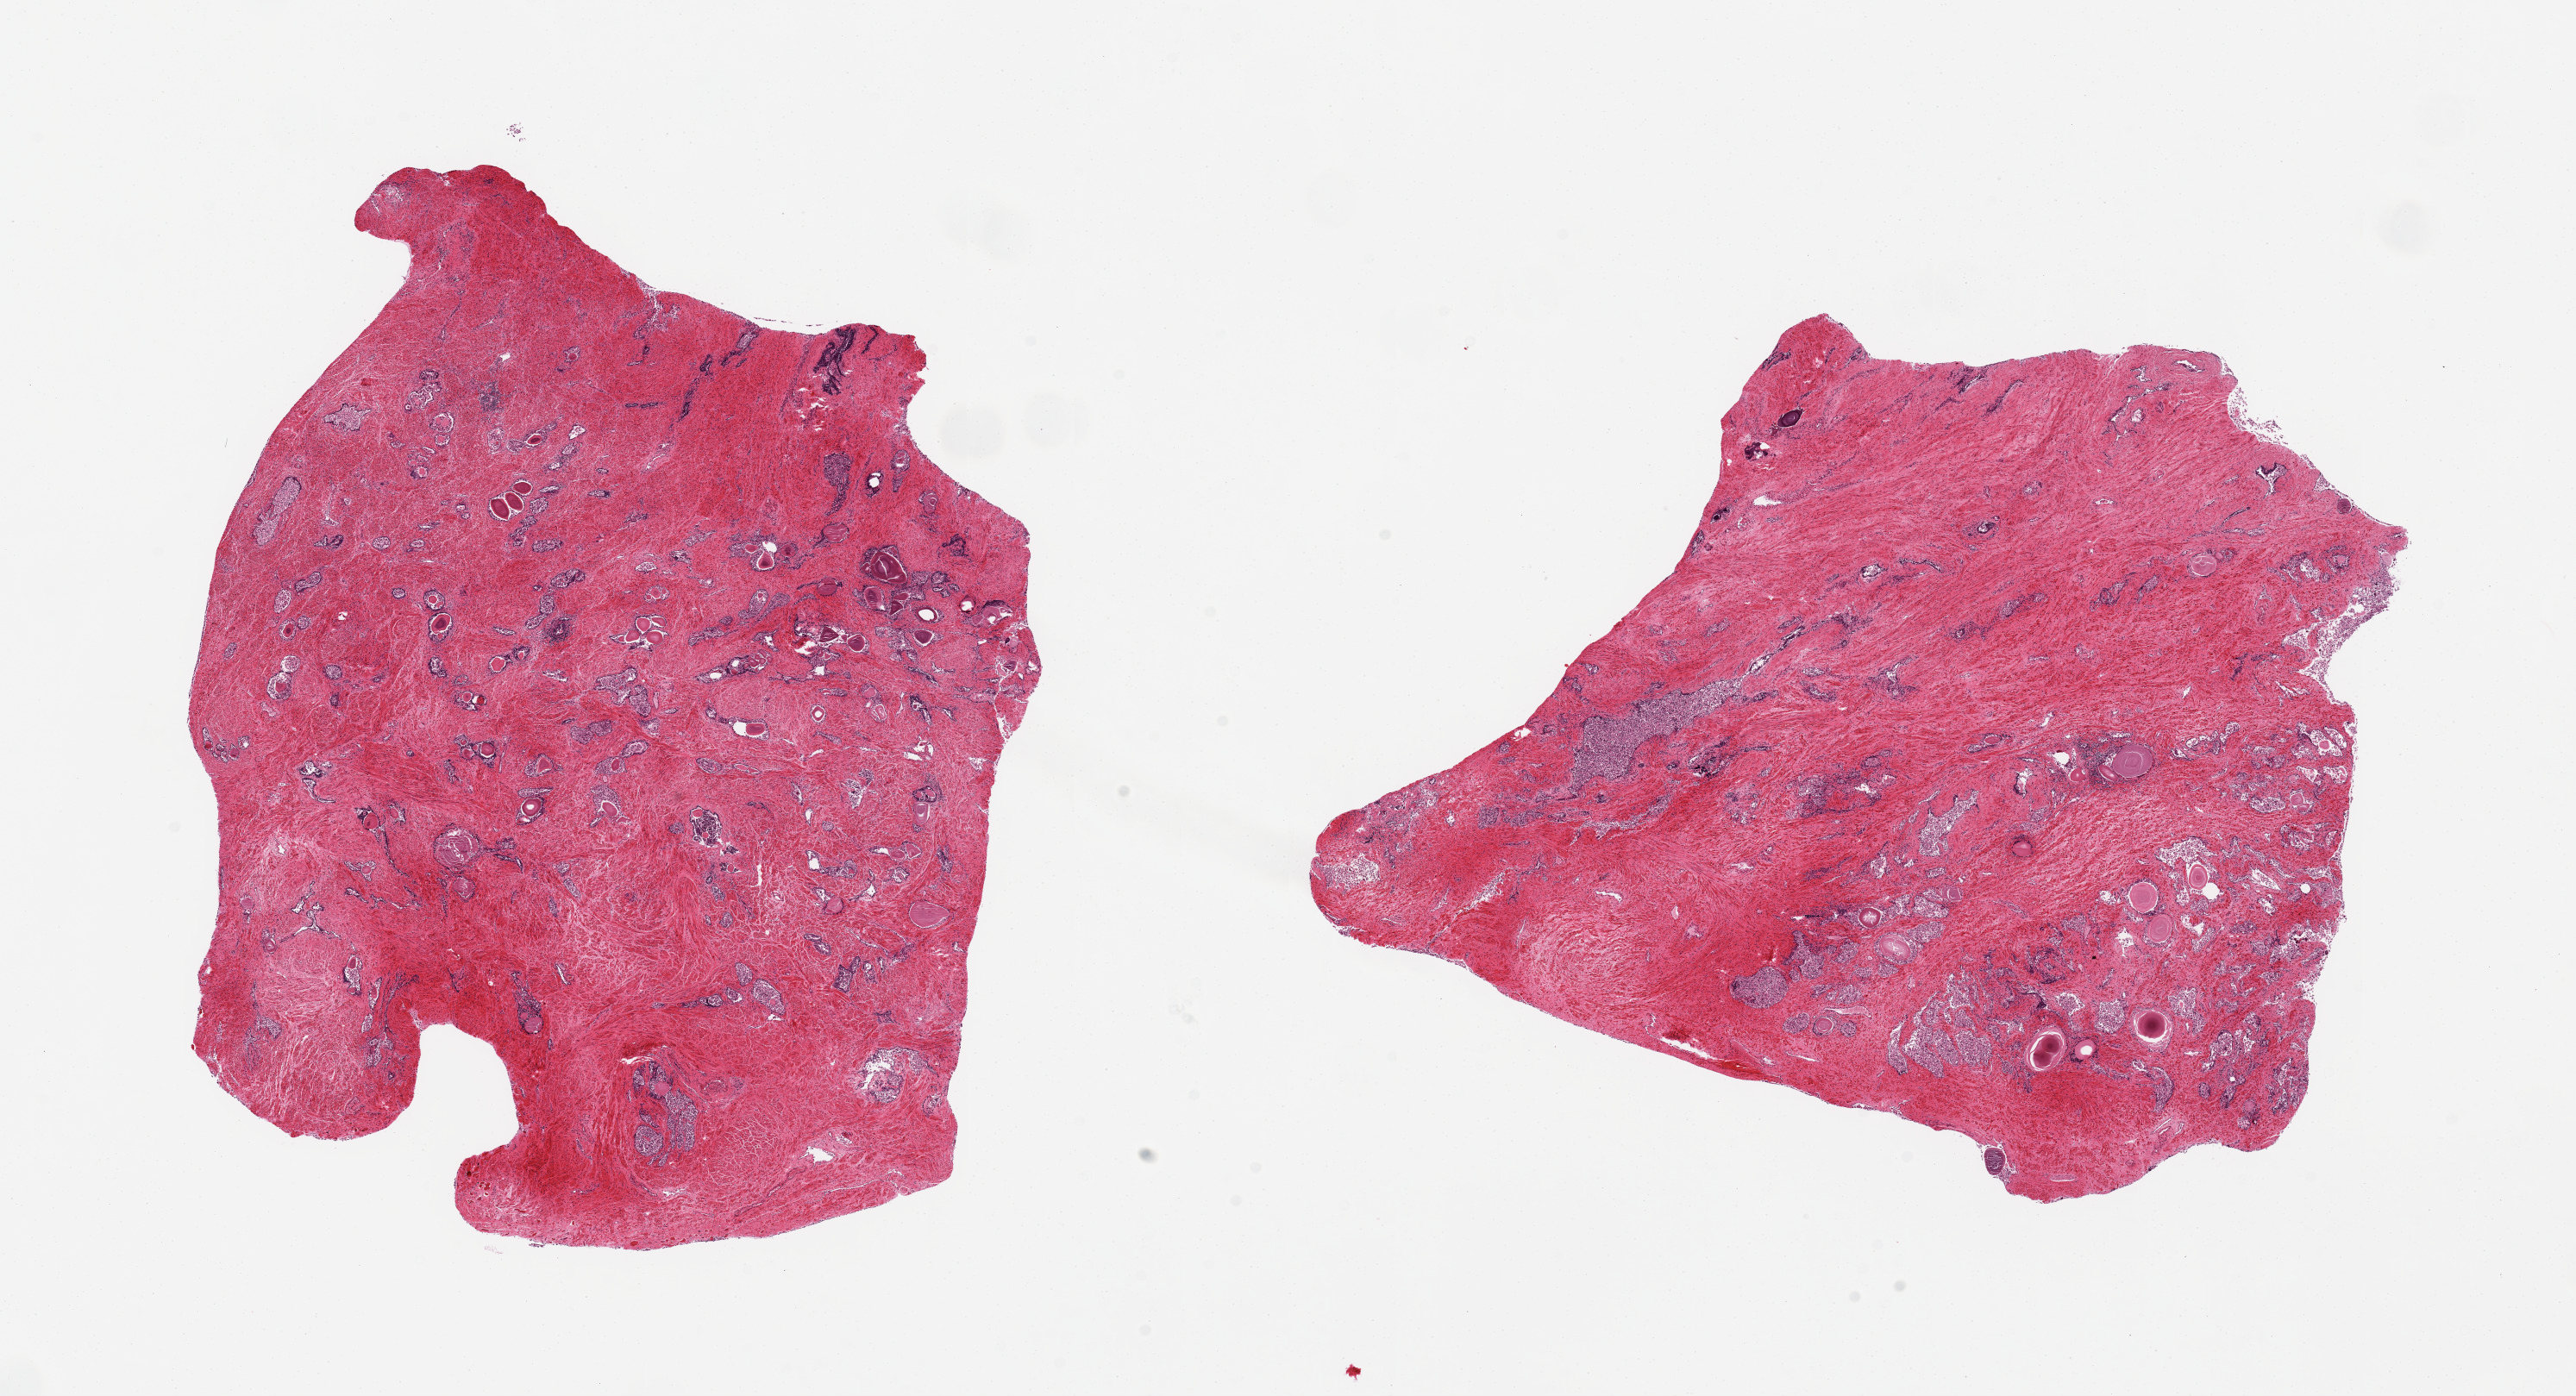
Digitized haematoxylin and eosin-stained section — whole scanned area (about 23.6 x 12.8 mm, acquisition: 20x scan) shown as a low-resolution overview, PAXgene-fixed paraffin-embedded (PFPE) section, target tissue: prostate, tissue donor sample. Donor: male.
Pathologist's review note for this sample: 2 pieces; glands autolyzed, stroma preserved.